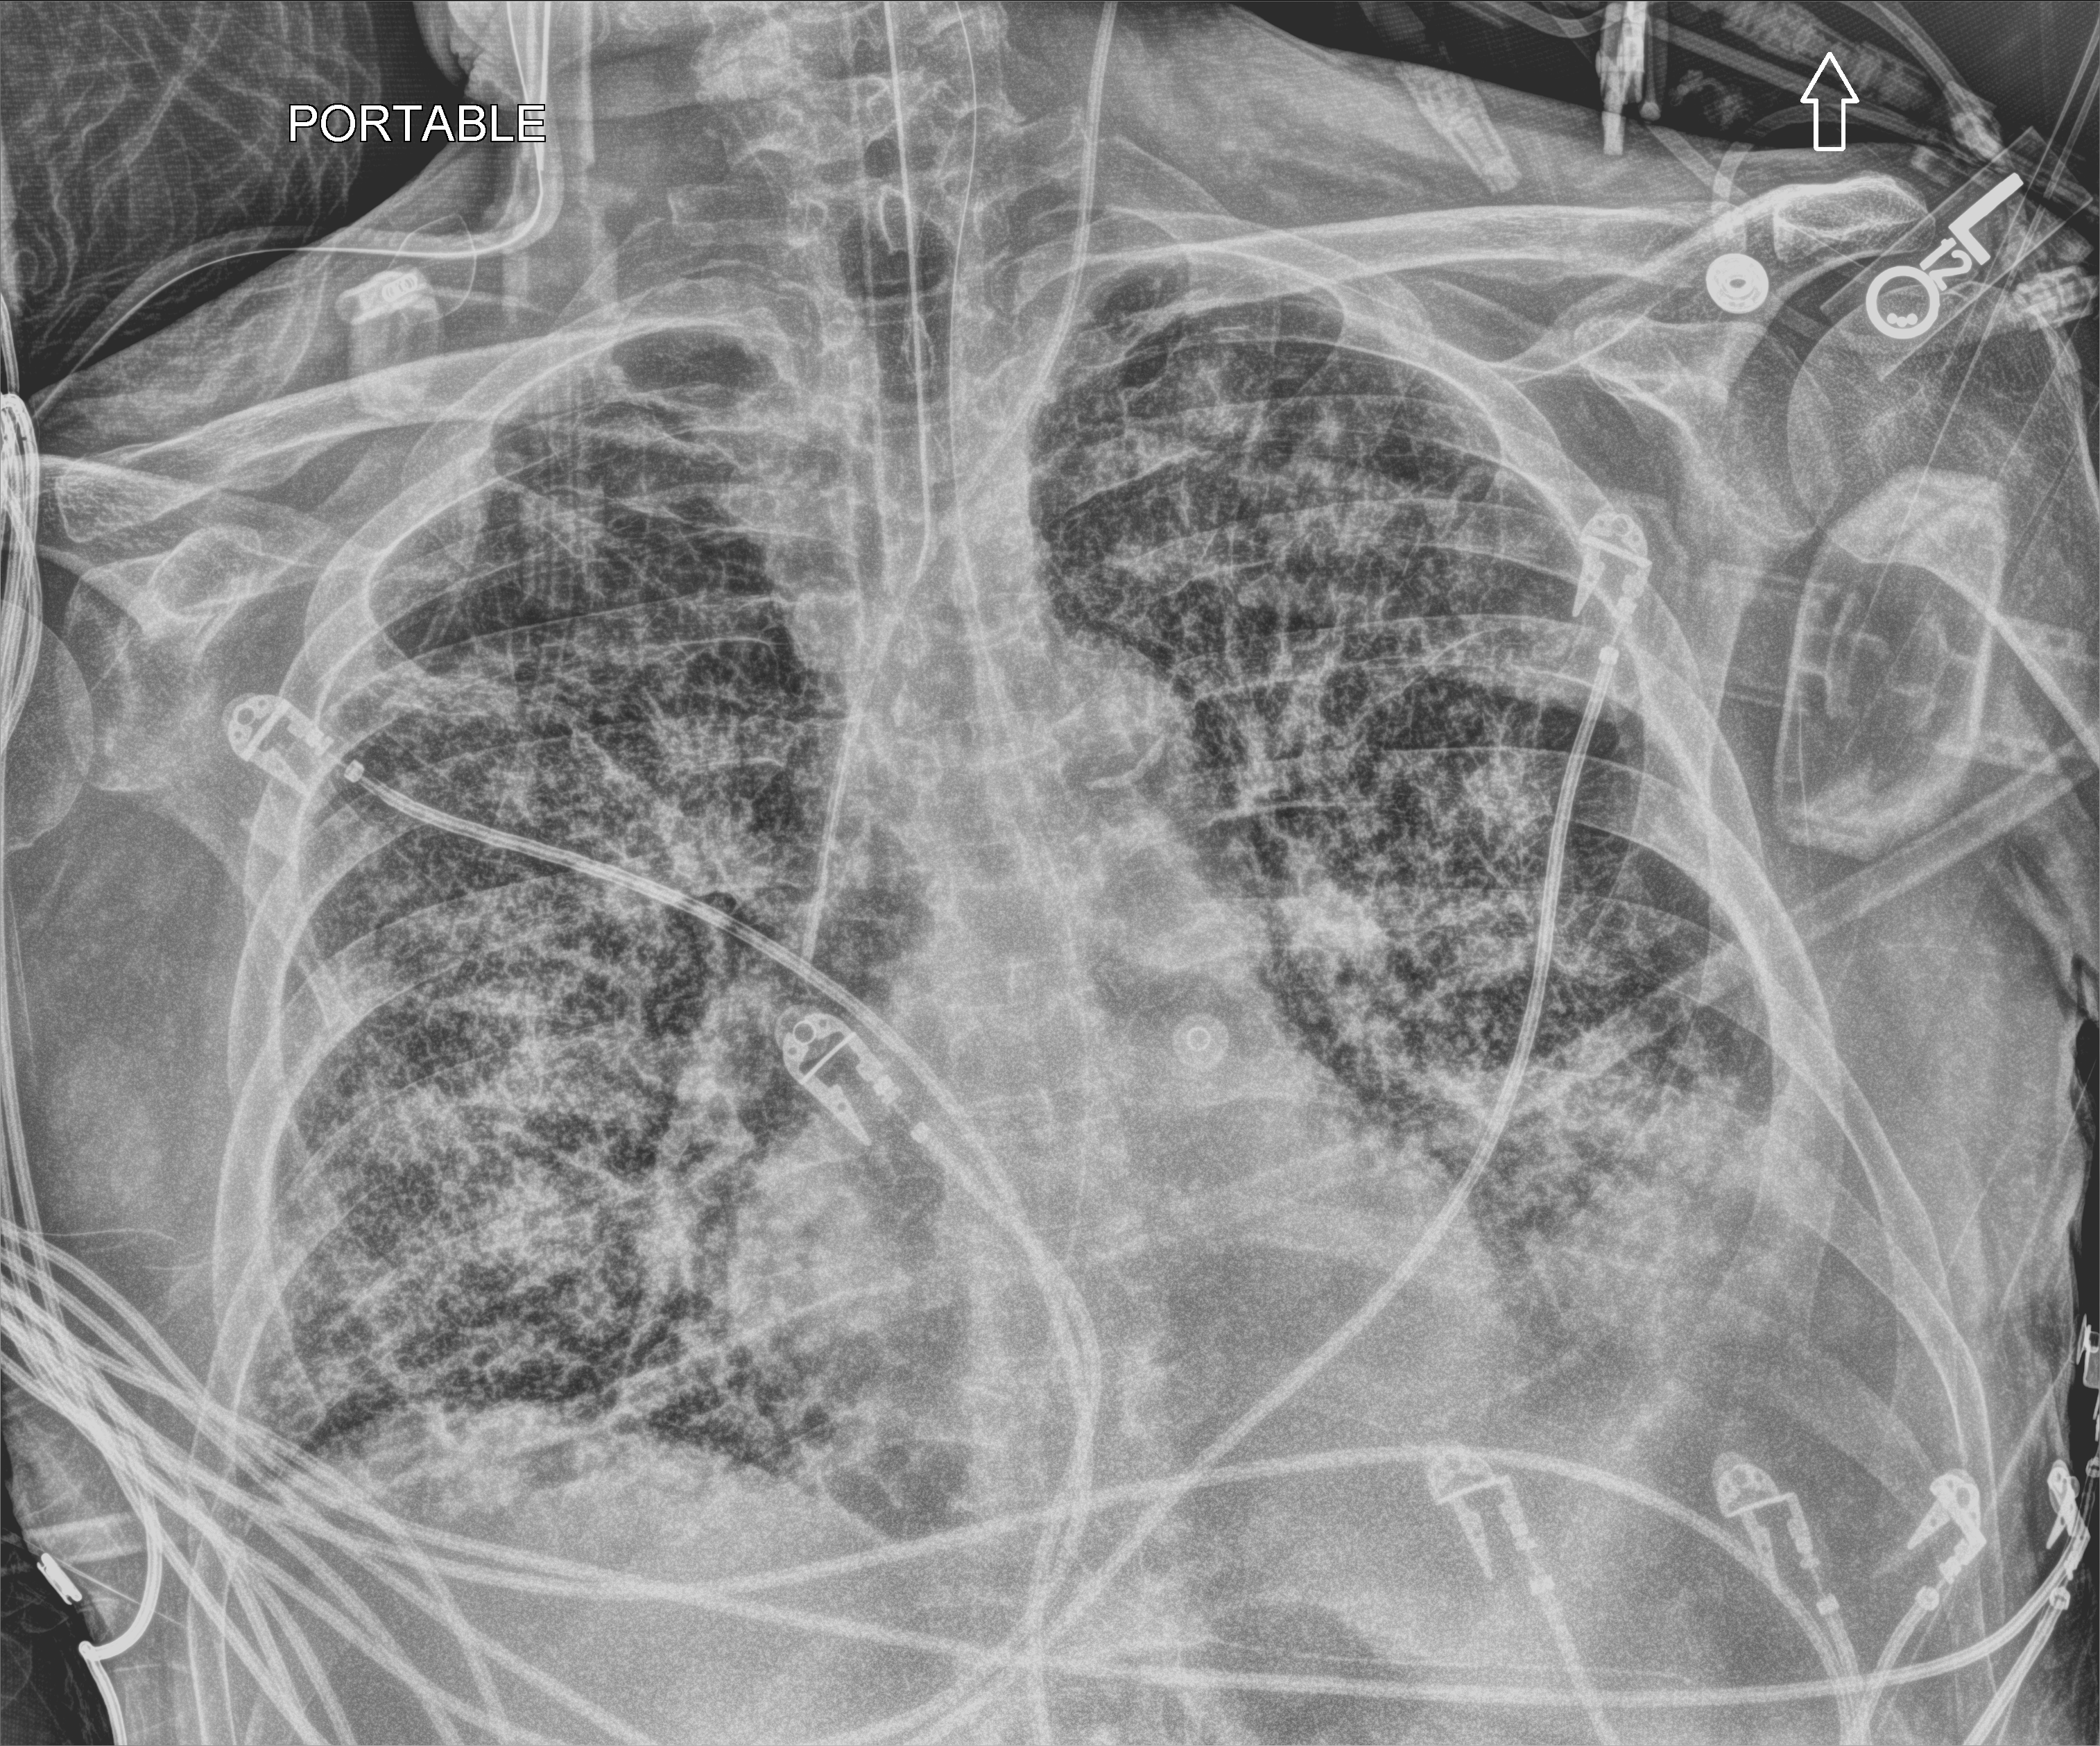
Chest X-ray (portable); anteroposterior (AP) projection. Patient hospitalised with COVID-19; male, aged 75–90 years.
From the hospital-stay record, not from the radiograph (when in the stay this image was taken is not recorded): diabetes (admission record): no; smoking status (admission record): never; admitted to intensive care during this hospital stay: yes.